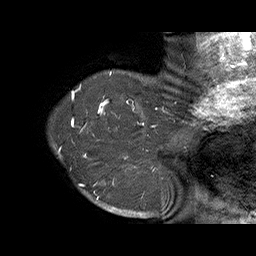
Breast MRI (dynamic contrast-enhanced), one sagittal slice. Dynamic contrast-enhanced series, time point 2 of 6 at this slice position (early post-contrast). 1.5 T. TE 4.5 ms, TR 32.4 ms. 3 mm slice thickness. 256 × 256 image matrix, field of view 180 × 180 mm. Female patient. Case-level facts recorded for this patient, not image findings: setting: breast cancer imaged before/during neoadjuvant chemotherapy; receptor status: HR-positive, HER2-negative.
Annotated regions visible in this slice (semi-automatically segmented with operator editing):
- analysis volume of interest (the breast-tissue region the enhancement analysis was run in; not a lesion): box from (x=71, y=128) to (x=159, y=202) px
- tumour enhancement mask (voxels above the 100 % enhancement threshold inside the analysis volume of interest): (x=72, y=128)–(x=156, y=202)